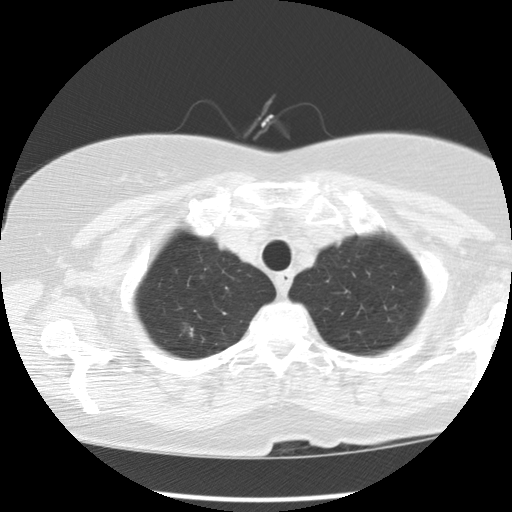
Low-dose screening chest CT, one axial slice. Position 110 of 122 along the scan axis. 120 kVp. Lung window (W 1500 / L -600 HU). 512 × 512 image matrix, field of view 329 × 329 mm.
Annotated regions visible in this slice (manually delineated by an expert):
- lesion 1 (tumor, upper lobe of right lung): bounding box [x1, y1, x2, y2] px = [182, 322, 194, 338]